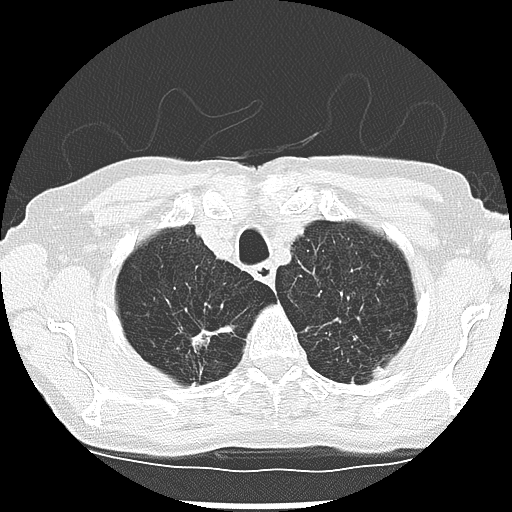
Low-dose screening chest CT, one axial slice. Slice 233 of 265 in the series (ordered by position). Reconstruction kernel LUNG. 120 kVp. Lung window (W 1500 / L -600 HU). 2.5 mm slice thickness. 512 × 512 image matrix.
Annotated regions visible in this slice (expert manual segmentation):
- lesion 2 (tumor, upper lobe of right lung): bounding box [x1, y1, x2, y2] px = [192, 330, 215, 349]